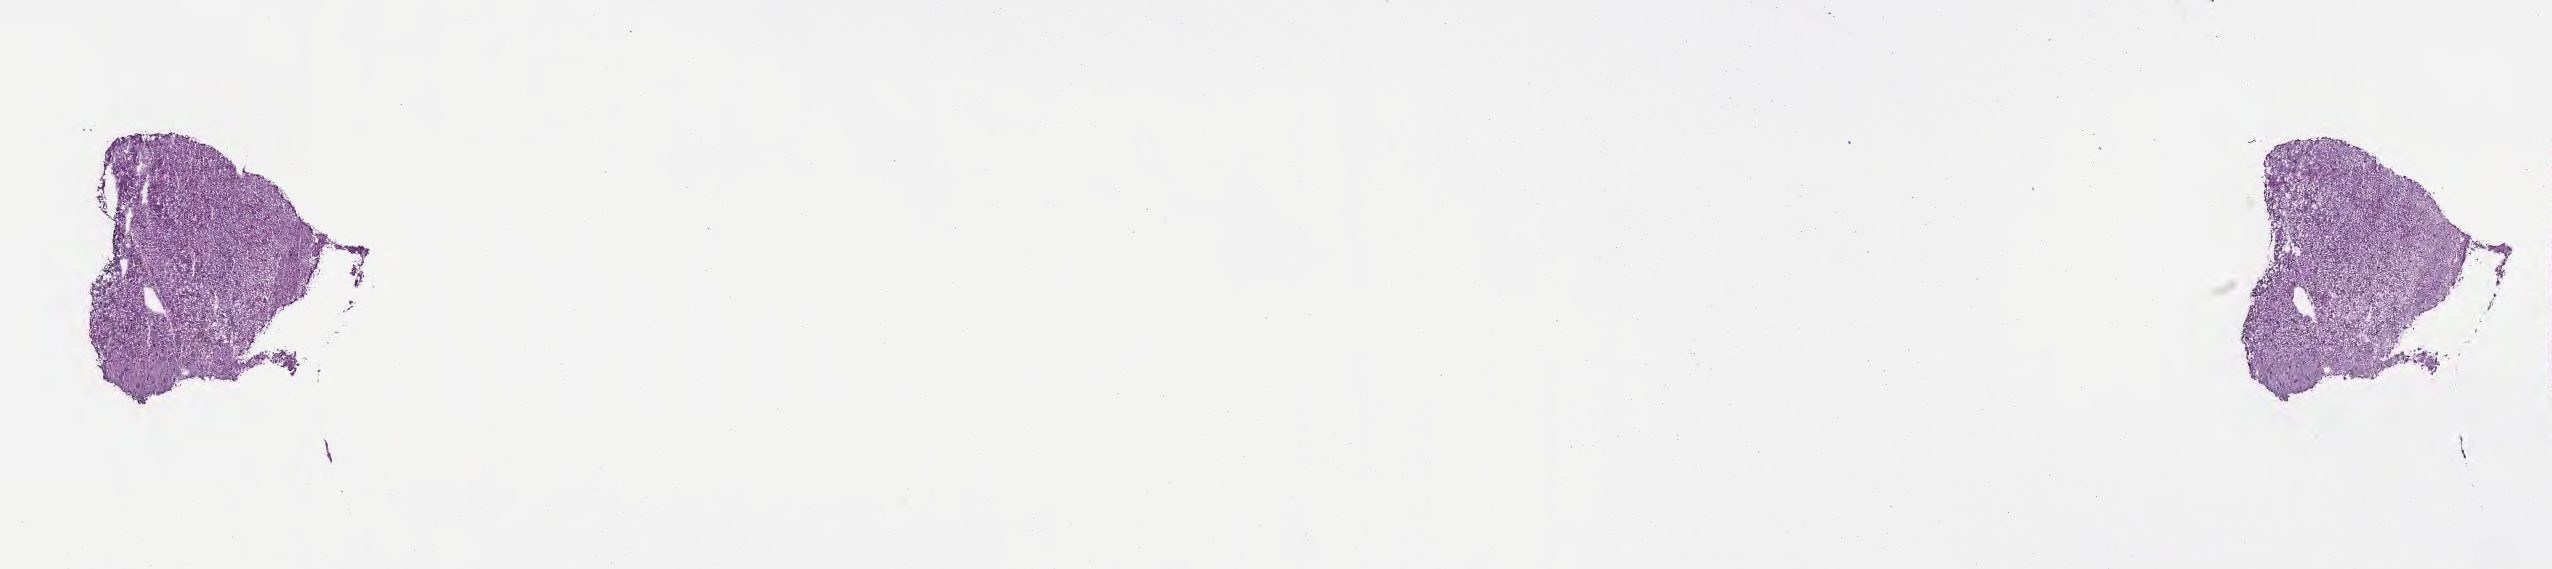
Whole-slide image, hematoxylin and eosin (H&E) stain of tumor tissue from the brain — low-resolution overview of the scanned area, about 20.6 x 4.6 mm; cryosection (OCT / tissue freezing medium). Patient: female, age 196 months (16 years 4 months).
Diagnosis: Glioma, malignant.